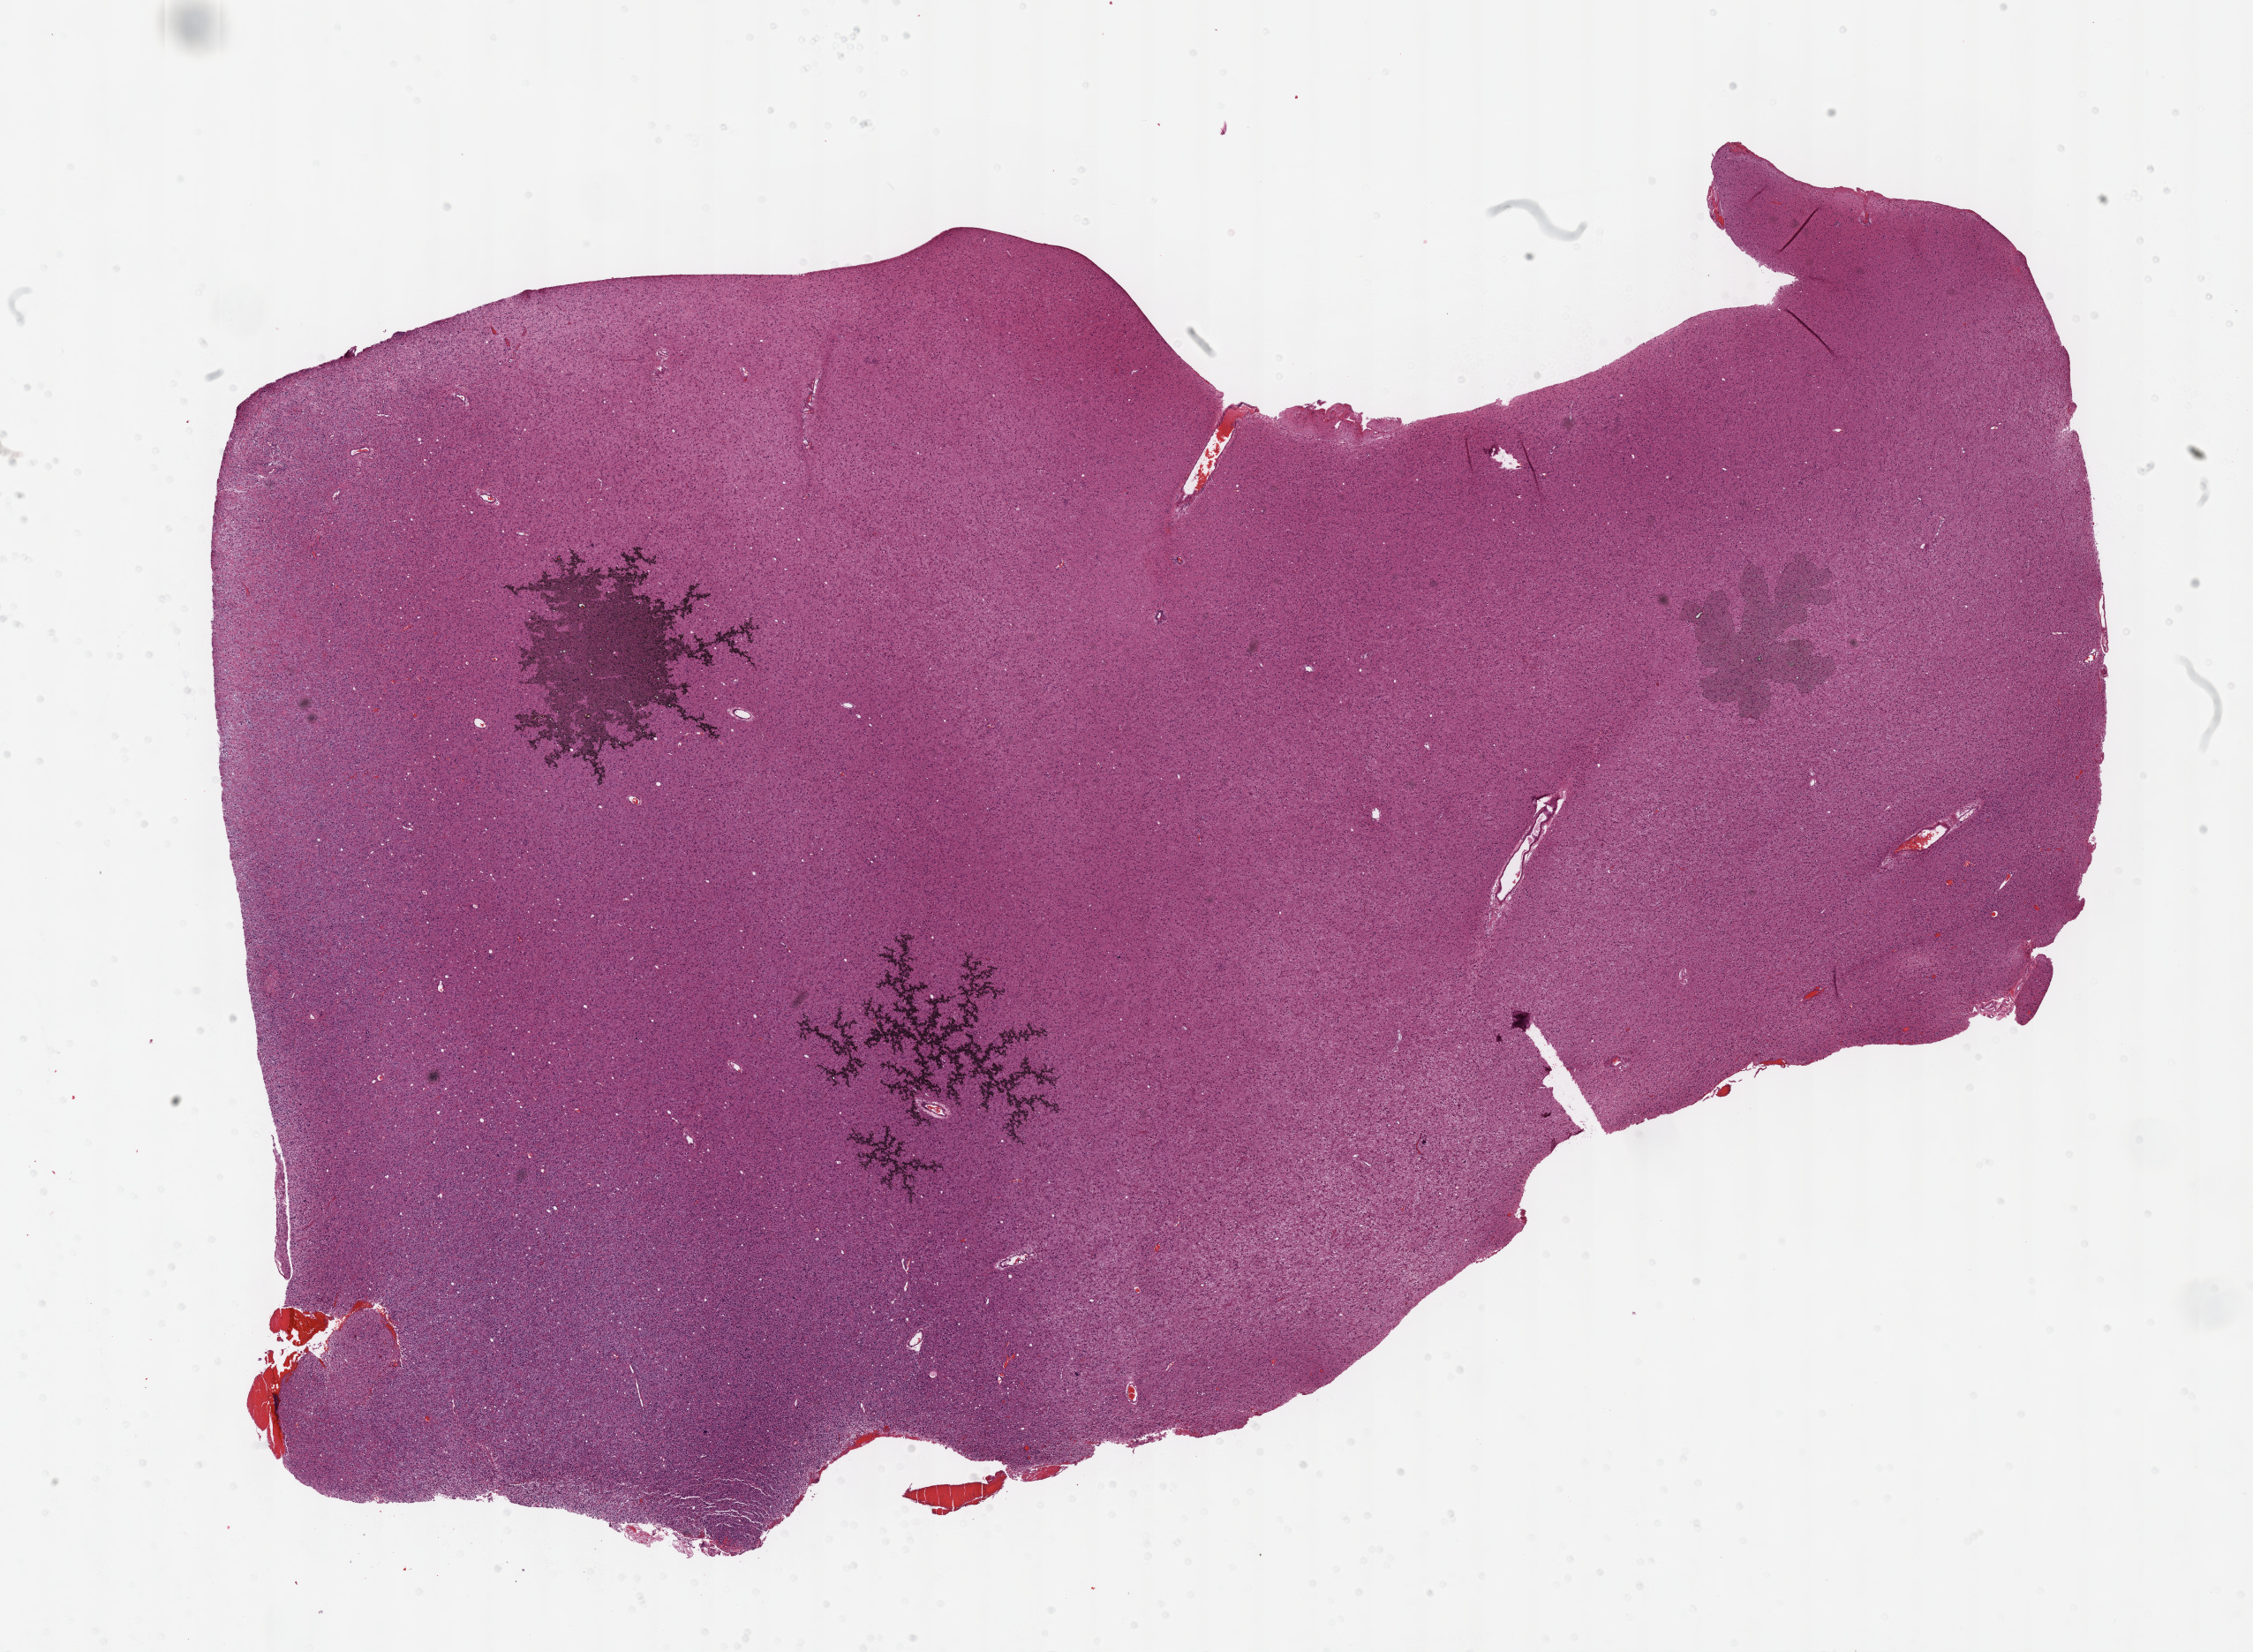
Digitized H&E tissue section (whole slide), whole scanned area (about 20.6 x 15.1 mm) shown as a low-resolution overview. Formalin-fixed paraffin-embedded (FFPE) diagnostic section. Sample: primary tumour, brain. Male, age 29 years at initial diagnosis.
Diagnosis: Mixed glioma (cerebrum).